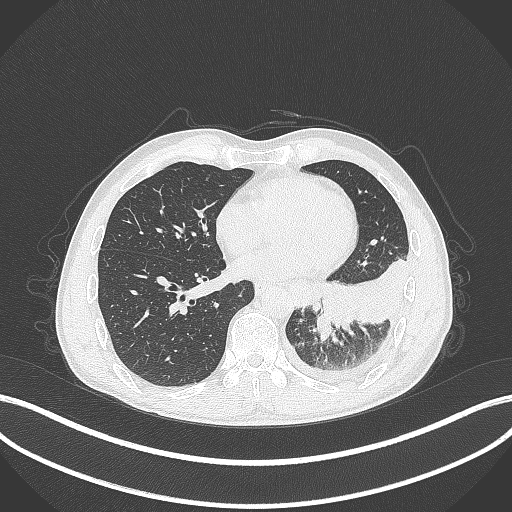
Chest CT, one axial slice. Position 111 of 295 along the scan axis. Reconstruction kernel B70f. 120 kVp. Lung window (W 1500 / L -600 HU). 1 mm slice thickness. 512 × 512 image matrix, field of view 400 × 400 mm. Patient: male, 47 years. From the clinical record (not read from this slice): clinical TNM (as recorded): T3 N1 M1c; histopathological grade: G3.
Annotated regions visible in this slice (rectangle marked by the reading radiologist):
- lung tumour (recorded histology: small cell carcinoma): bounding box (x1, y1, x2, y2) in pixels: (314, 313, 335, 342)